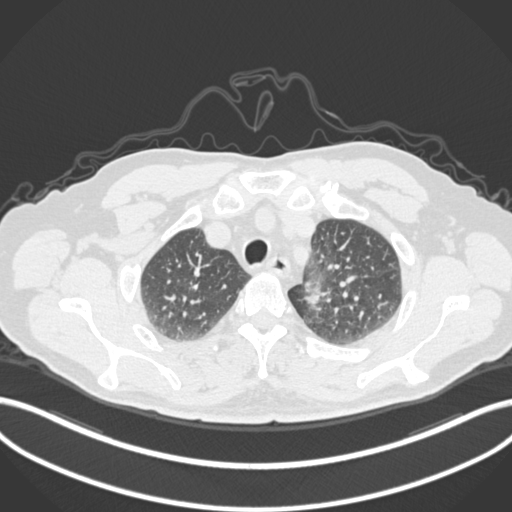
Chest CT, one axial slice; position 268 of 306 along the scan axis; reconstruction kernel B30f; lung window (W 1500 / L -600 HU); 512 × 512 image matrix, field of view 400 × 400 mm. Male patient, age 64 years. Case-level facts recorded for this patient, not image findings: clinical TNM (as recorded): T1c N0 M0.
Structures marked on this image (rectangle marked by the reading radiologist):
- lung tumour (recorded histology: adenocarcinoma): bounding box <302,278,335,312> (left, top, right, bottom; pixels)